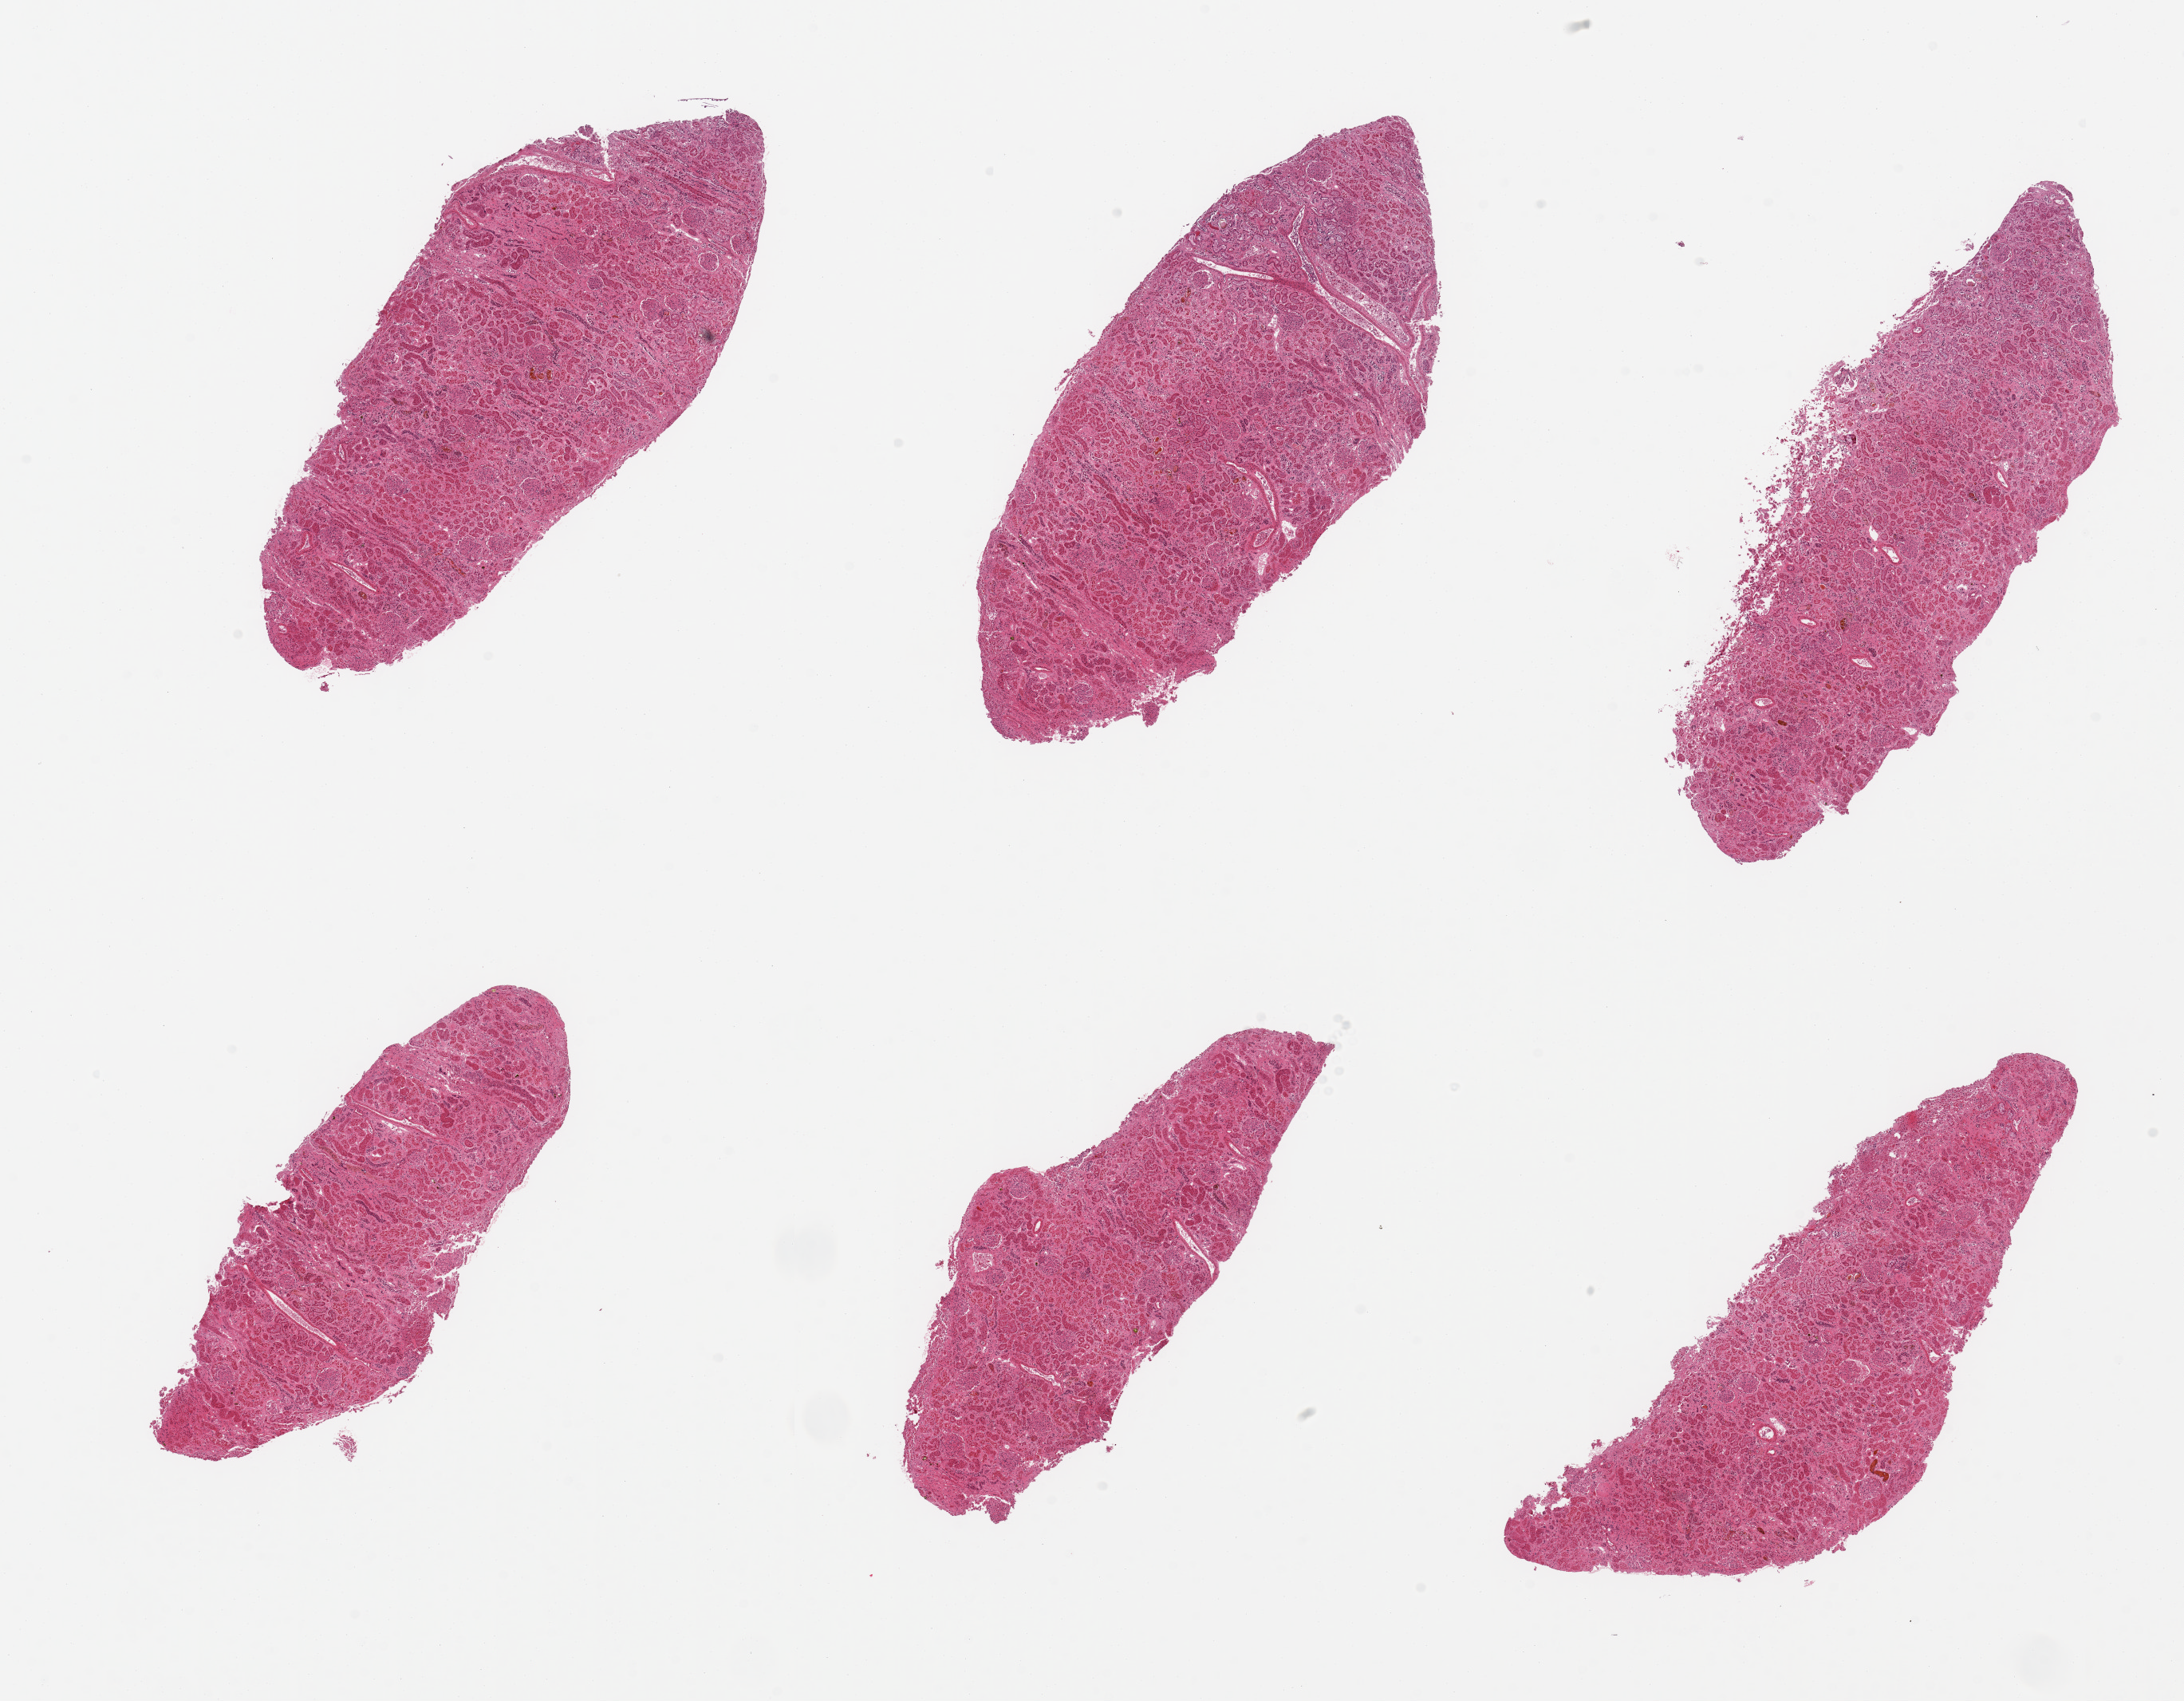
Whole-slide image, haematoxylin and eosin stain, low-resolution overview of the scanned area, about 21.7 x 16.9 mm (from a 20x scan). PAXgene-fixed, paraffin-embedded tissue. Sampled site (target tissue): renal cortex. Tissue donor sample. Male donor.
* pathologist's review note for this sample: 6 pieces; moderate to severe tubular autolysis (sloughed tubular epithelium) and tubular bile casts; diffuse membranoproliferative glomerulonephritis (mesangial cell proliferation and capillary wall thickening)- likely secondary